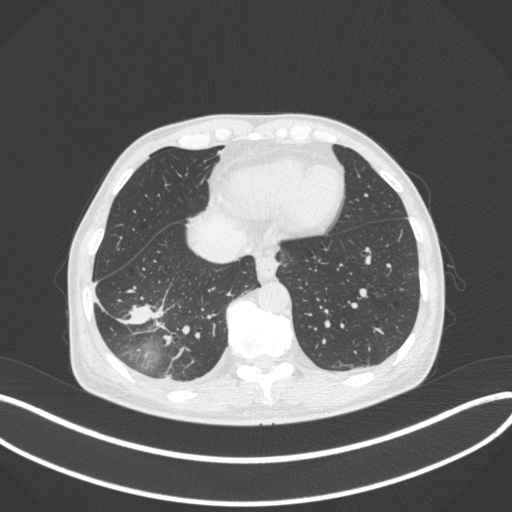
Chest CT, one axial slice. Slice 97 of 385 in the series (ordered by position). Reconstruction kernel B31f. Lung window (W 1500 / L -600 HU). 1 mm slice thickness. 512 × 512 image matrix. Male patient, age 64 years. From the clinical record (not read from this slice): clinical TNM (as recorded): T3 N0 M0; histopathological grade: G2-3.
Structures marked on this image (bounding box drawn by a radiologist):
- lung tumour (recorded histology: adenocarcinoma): bounding box [x1, y1, x2, y2] px = [114, 294, 170, 335]